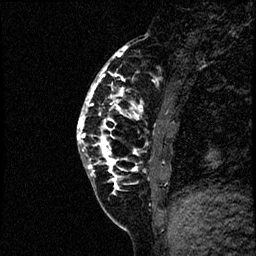
Breast MRI (dynamic contrast-enhanced), one sagittal slice. Slice 19 of 60 in the series (ordered by position). Dynamic contrast-enhanced study with each time point stored as its own series, time point 2 of 4 at this slice position (early post-contrast, ordered by acquisition time). 1.5 T. TE 4.2 ms, TR 17.6 ms. 2 mm slice thickness. 256 × 256 image matrix, field of view 200 × 200 mm. Patient: female, 40 years. From the clinical record (not read from this slice): setting: breast cancer imaged before/during neoadjuvant chemotherapy; receptor status: HER2-positive.
Annotated regions visible in this slice (semi-automatic segmentation, software-assisted and operator-edited):
- analysis volume of interest (the breast-tissue region the enhancement analysis was run in; not a lesion): bounding box (x1, y1, x2, y2) in pixels: (78, 56, 197, 205)
- tumour enhancement mask (voxels above the 100 % enhancement threshold inside the analysis volume of interest): (78, 65, 144, 182)